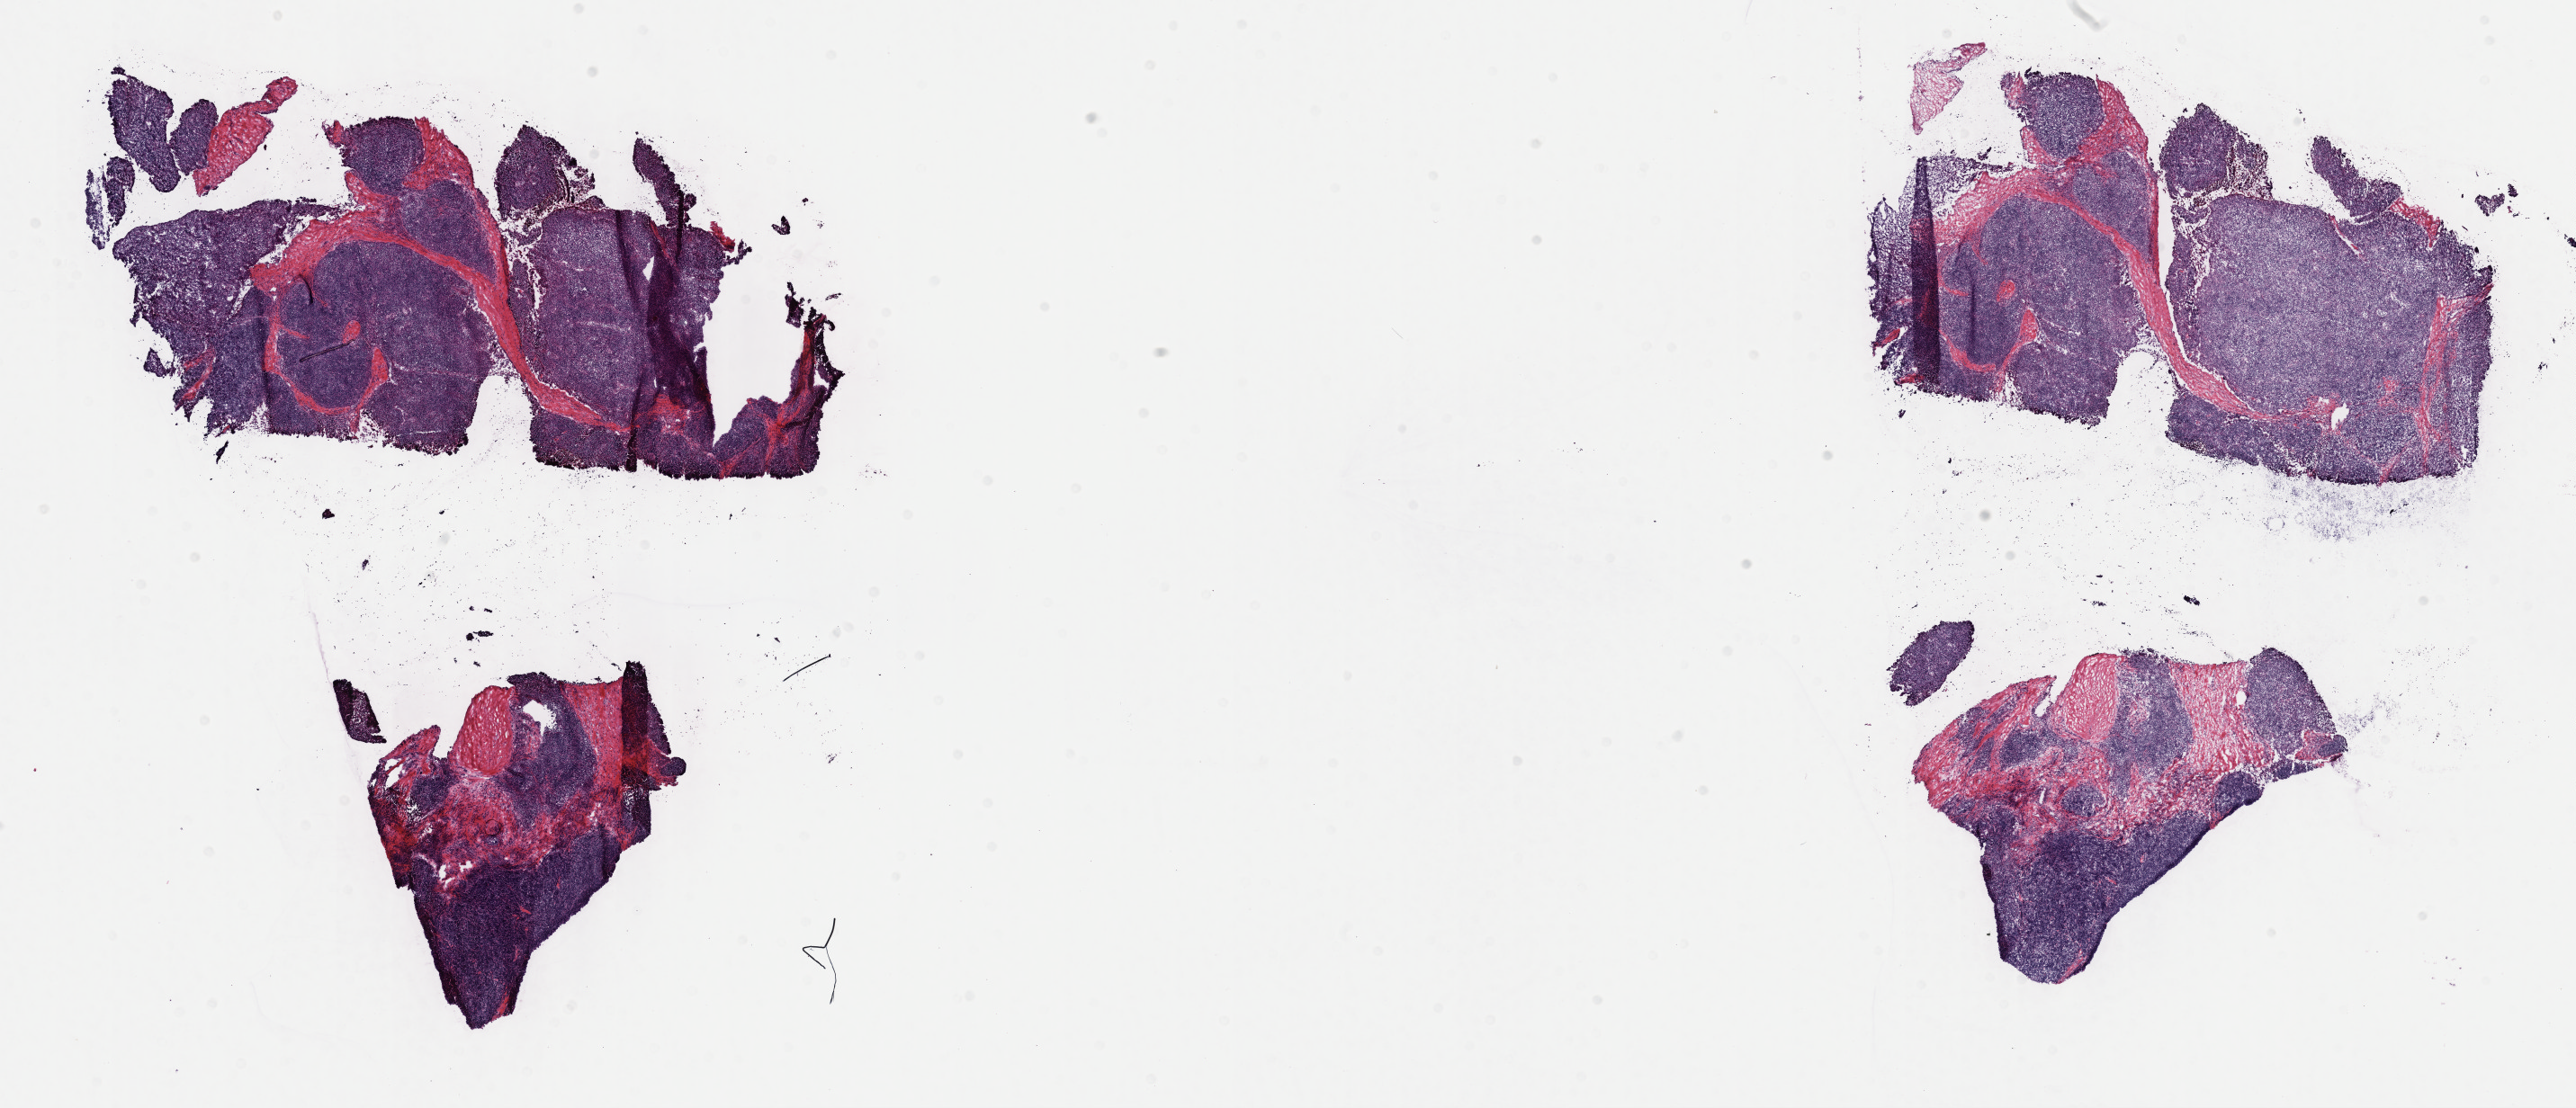
H&E-stained whole-slide image — a low-resolution overview of the entire scanned area, about 23.2 x 10.0 mm. Frozen section from the top of the tissue portion. Primary tumour sample from the thymus. Female patient; age at initial diagnosis 45 years. Slide review estimates, as recorded: tumour cells 80%, tumour nuclei 80%, normal cells 0%, stromal cells 20%, necrosis 0%. Infiltration values recorded for this section: lymphocyte infiltration 2%, monocyte infiltration 1%, neutrophil infiltration 2%.
* histologic diagnosis: Thymoma, type B2, malignant